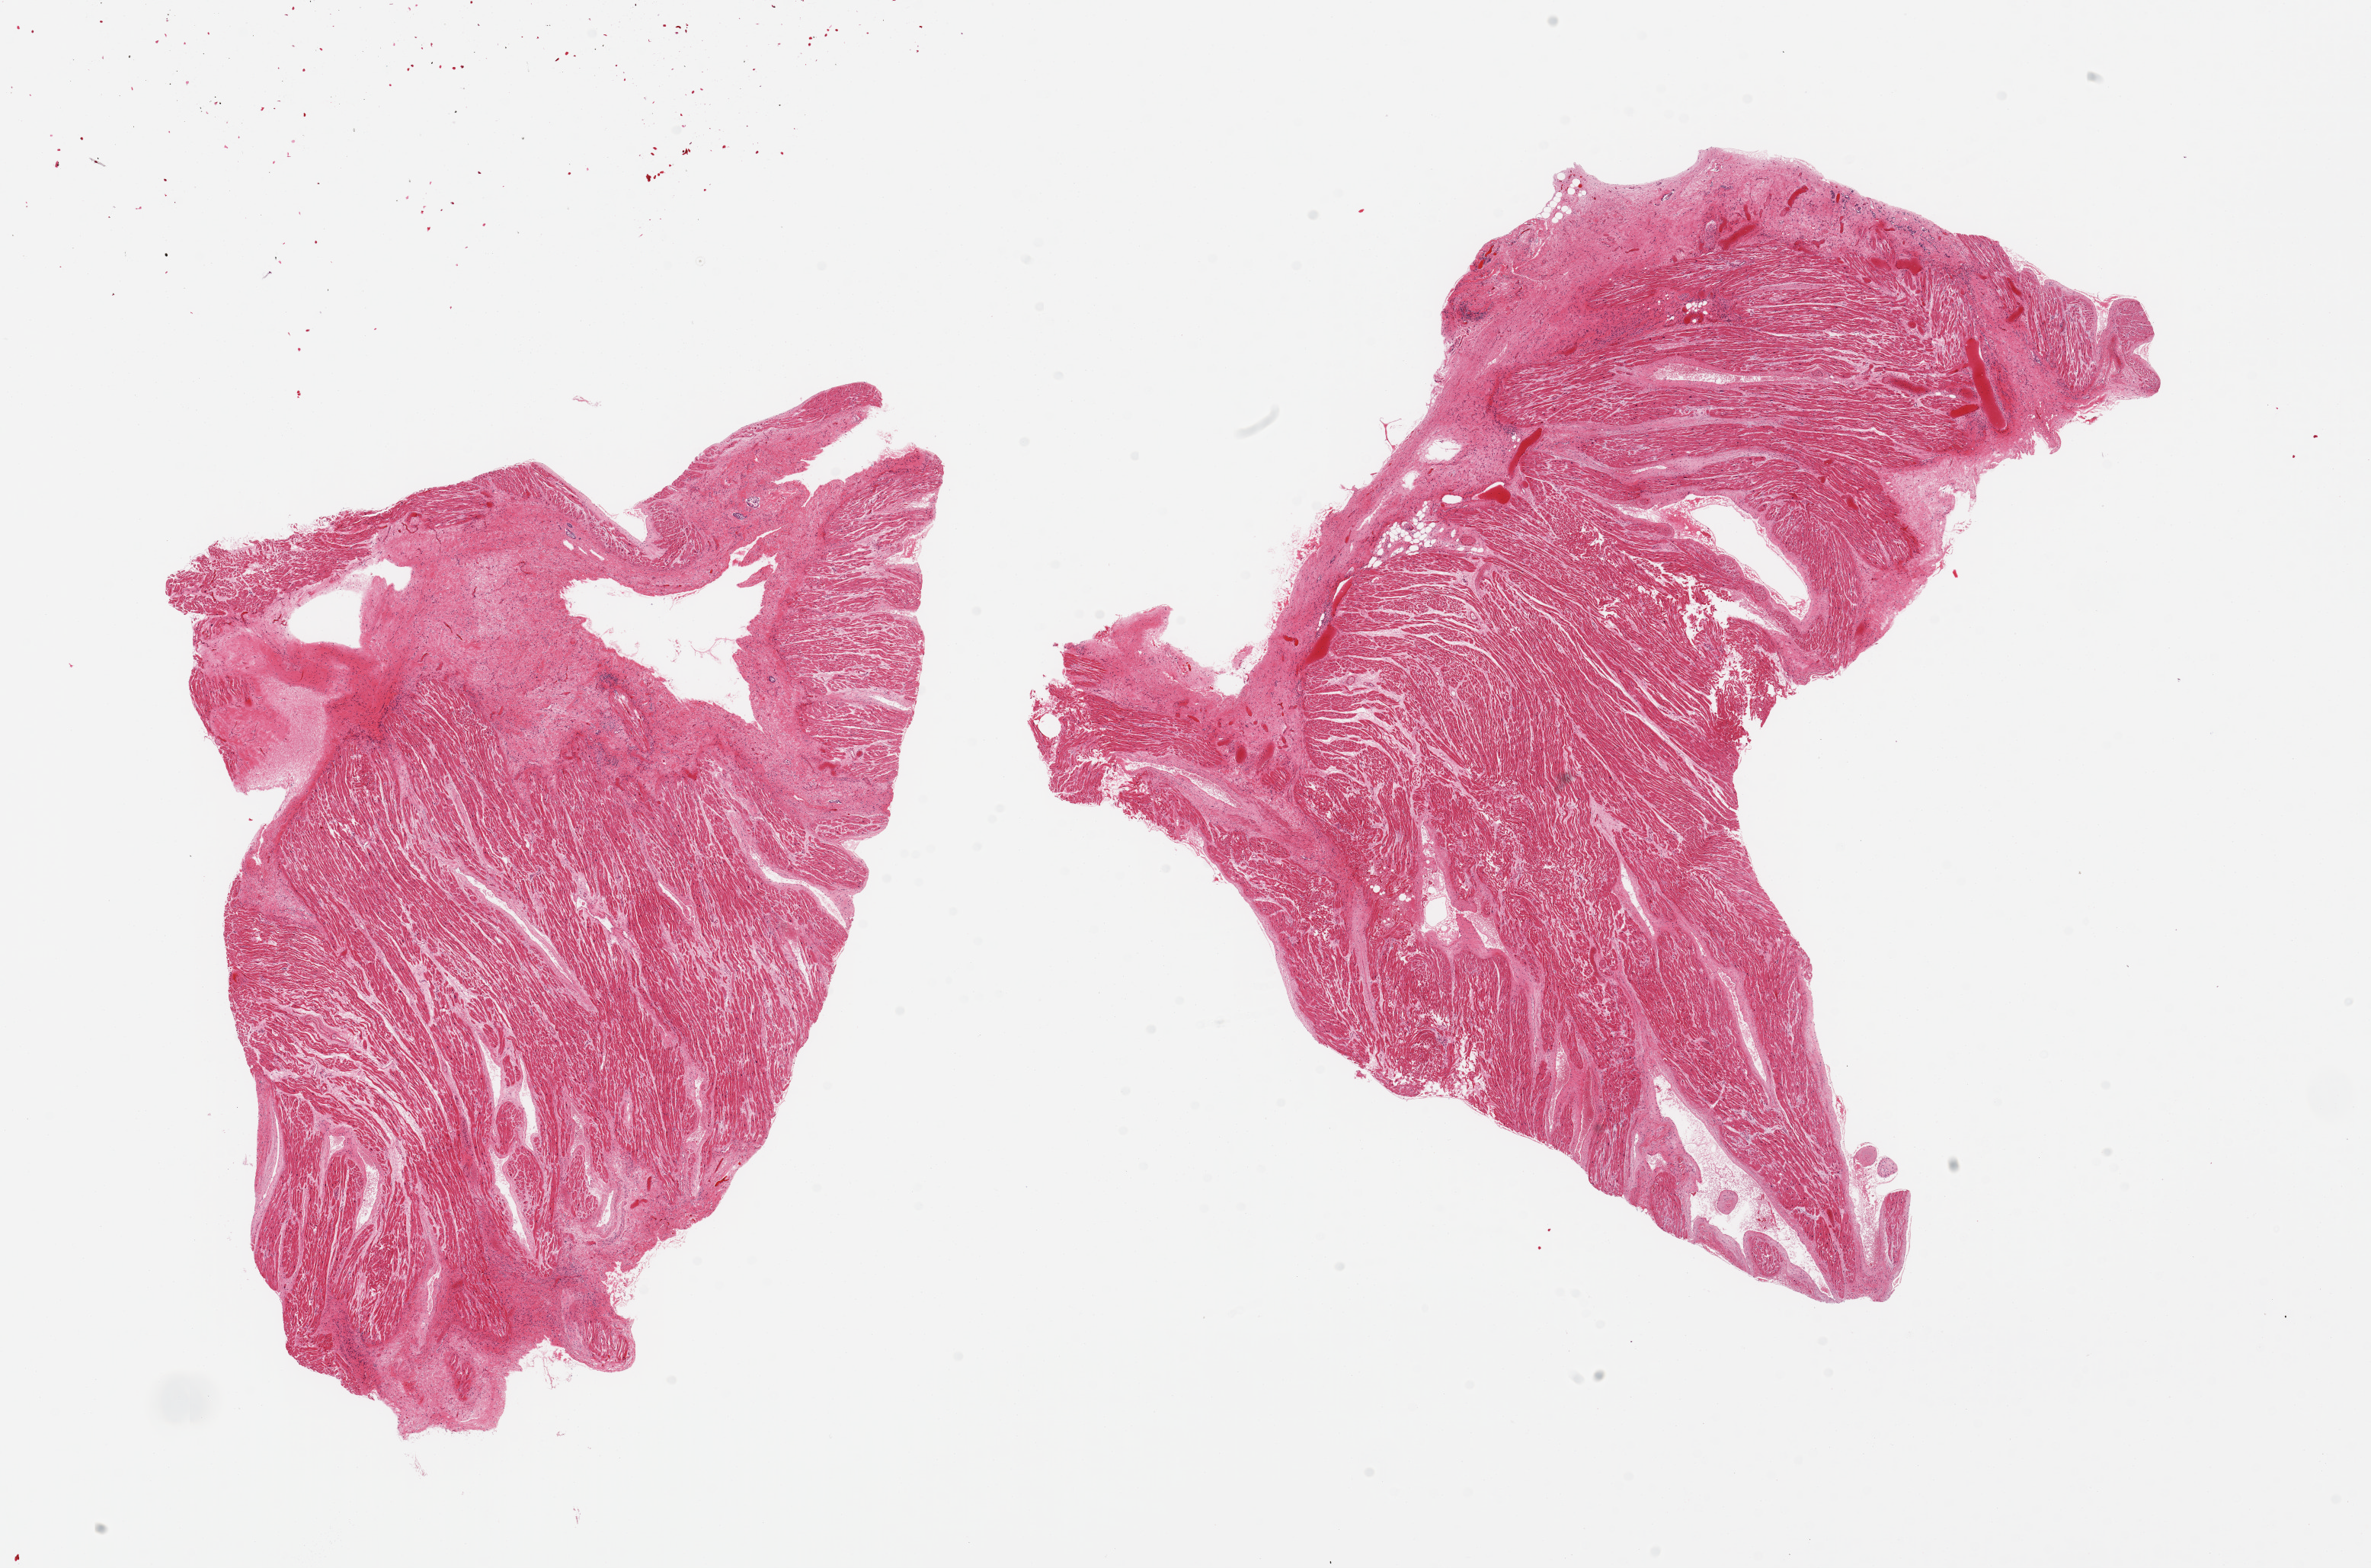
Hematoxylin and eosin (H&E) whole-slide image, brightfield — shown as a low-resolution overview of the whole scanned area (about 24.6 x 16.3 mm, from a 20x scan); PAXgene-fixed paraffin-embedded (PFPE) section; section of auricular appendage (target tissue); tissue donor sample.
Reviewer comment on this tissue sample: 2 pieces; 10% fibrous content.